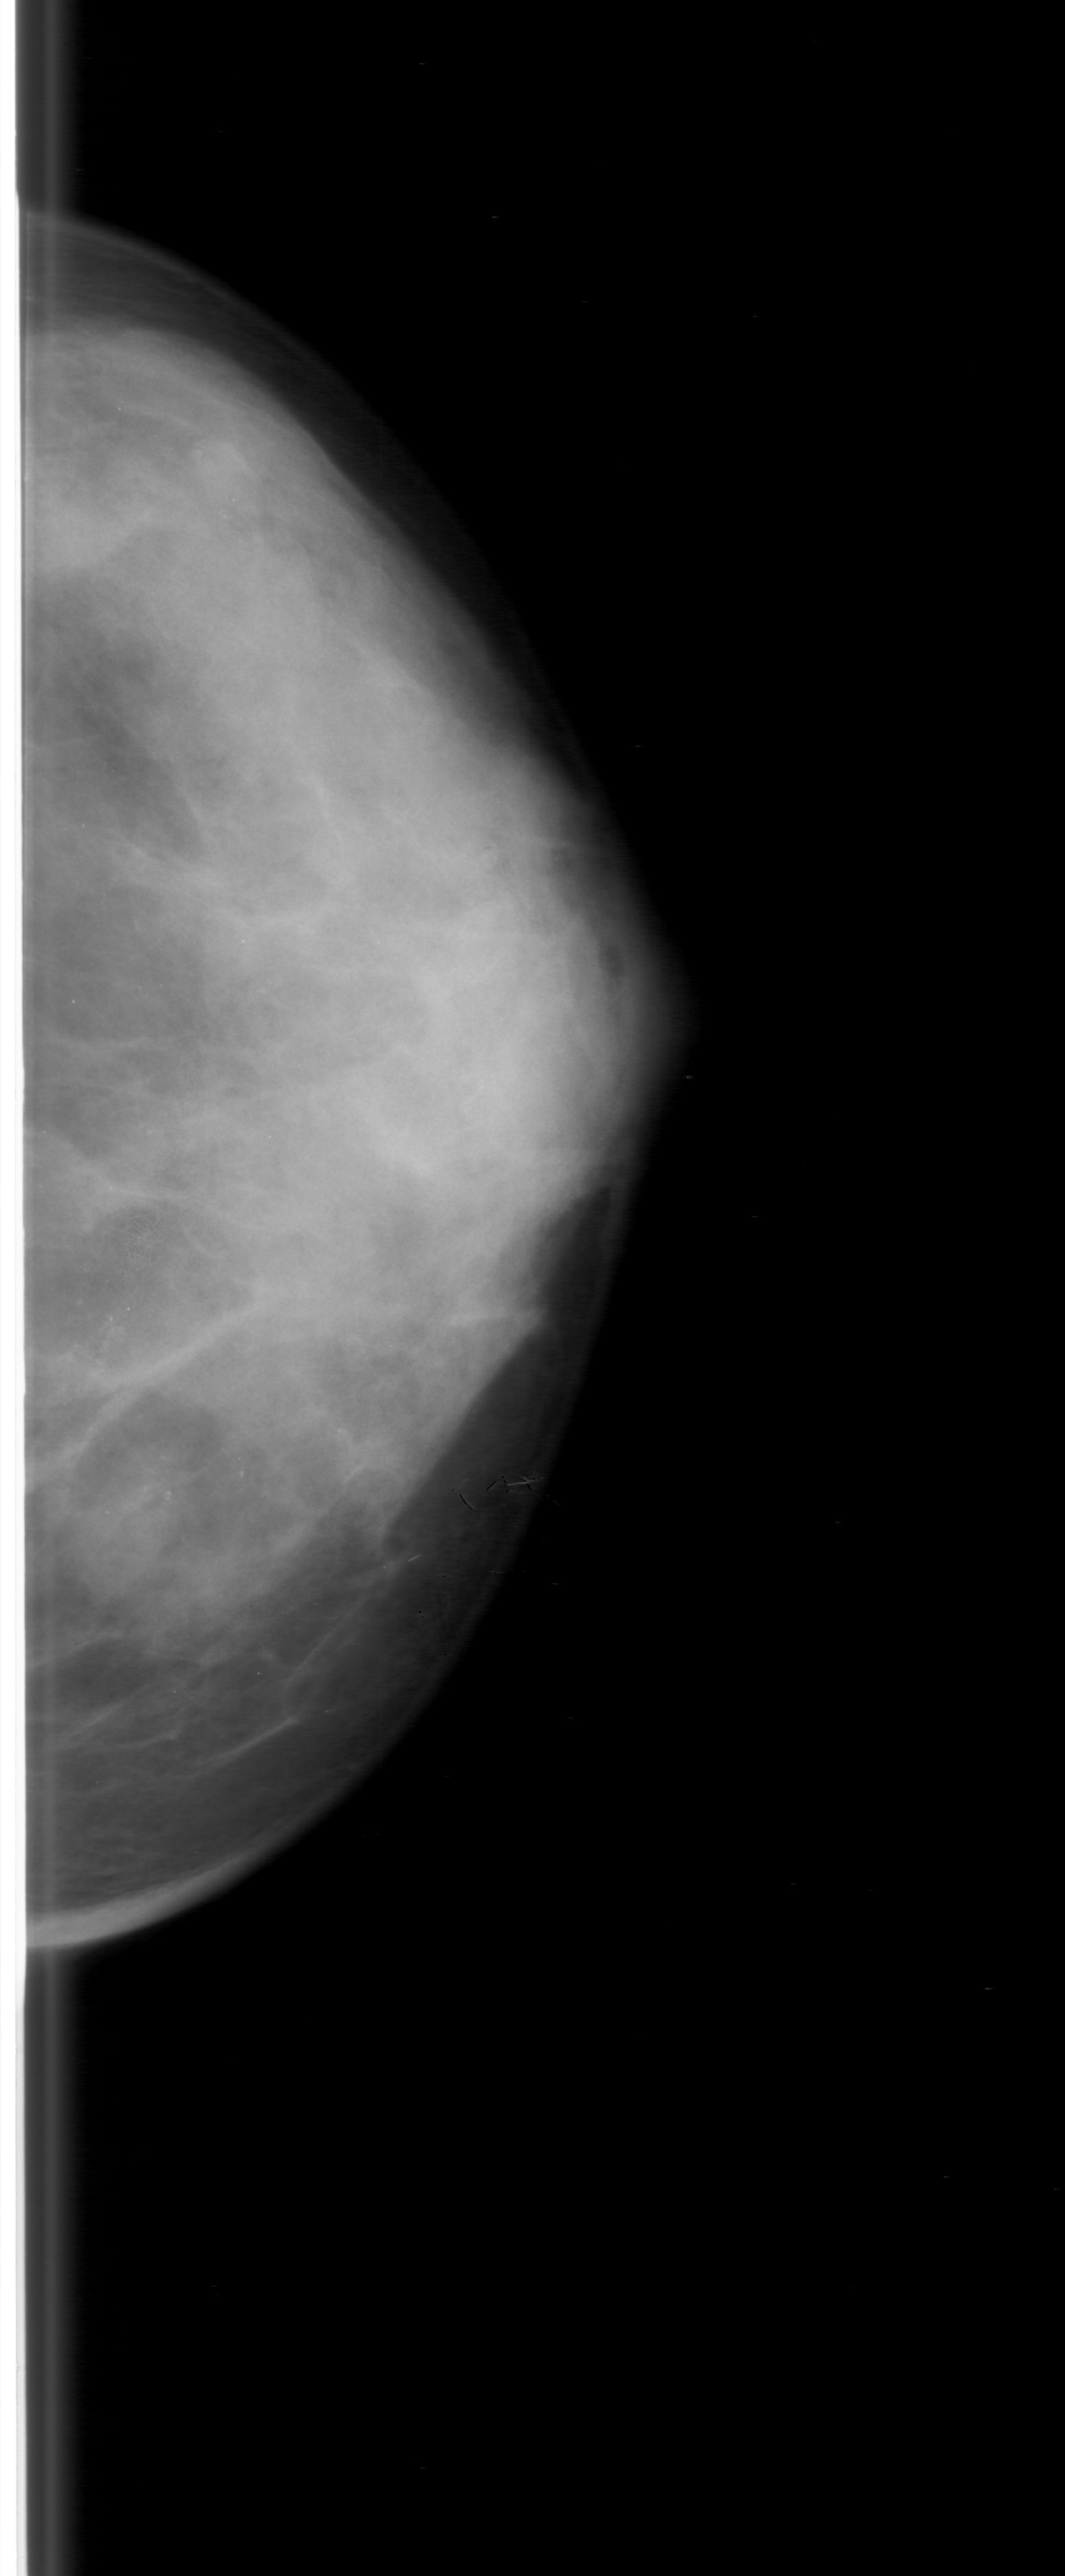
Mammogram (digitized film); left breast; craniocaudal (CC) view; breast composition: heterogeneously dense (BI-RADS density category 3 of 4).
- Calcifications, morphology fine linear branching, distribution linear; BI-RADS assessment category 3; pathology (as recorded): malignant.